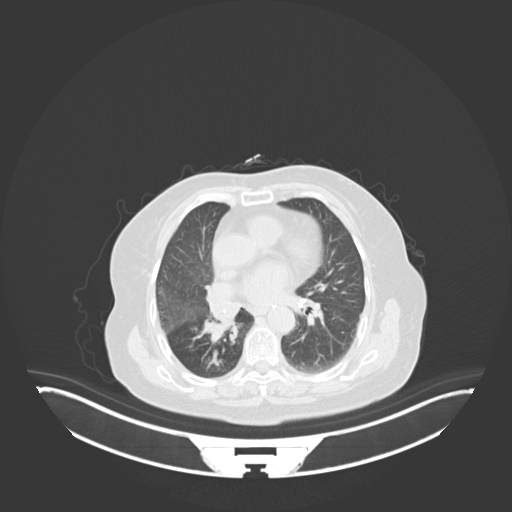
Chest CT, one axial slice. Position 27 of 76 along the scan axis. Reconstruction kernel B30f. 120 kVp. Lung window (W 1500 / L -600 HU). 3 mm slice thickness. 512 × 512 image matrix. Patient: female, 75 years. Case-level facts recorded for this patient, not image findings: clinical TNM (as recorded): T1b N0 M1a; histopathological grade: G1.
Structures marked on this image (bounding box drawn by a radiologist):
- lung tumour (recorded histology: squamous cell carcinoma): box from (x=205, y=304) to (x=239, y=344) px